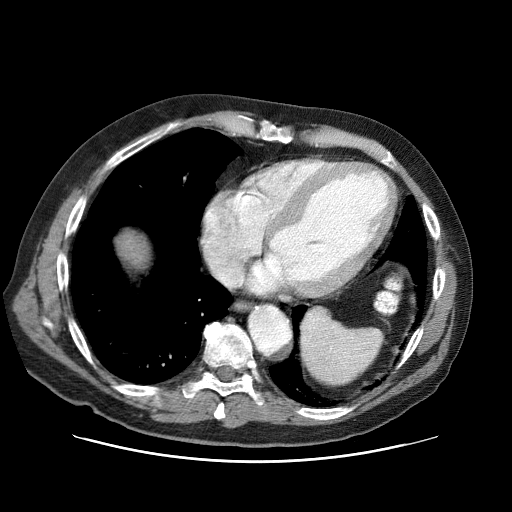
Contrast-enhanced abdominal CT (liver protocol), one axial slice; slice 74 of 87 in the series (ordered by position); reconstruction kernel STANDARD; one of 3 acquisitions stored at this slice position; soft-tissue window (W 400 / L 40 HU); 2.5 mm slice thickness; 512 × 512 image matrix, field of view 400 × 400 mm. From the clinical record (not read from this slice): diagnosis: hepatocellular carcinoma (patient treated with transarterial chemoembolisation; whether this scan precedes or follows treatment is not stated here); TNM stage (as recorded): Stage-IIIA; Child-Pugh class: A; tumour differentiation: well differentiated; tumour size: 6 cm.
Annotated regions visible in this slice (semi-automatic segmentation, software-assisted and operator-edited):
- liver parenchyma outside the tumour (the mass and vessels are separate outlines, so this box may not span the whole liver): box from (x=118, y=232) to (x=149, y=268) px